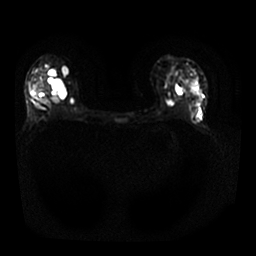
Breast MRI, one axial slice; slice 14 of 25 in the series (ordered by position); diffusion-weighted series; image 2 of 4 stored at this slice position (different b-values; order by instance number); 1.5 T; 256 × 256 image matrix. Female patient.
Structures marked on this image (expert manual segmentation):
- tumour on diffusion-weighted imaging: box from (x=31, y=75) to (x=52, y=95) px